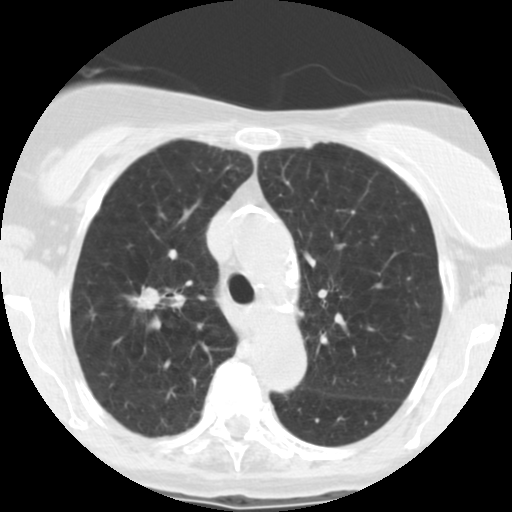
Low-dose screening chest CT, axial slice, baseline screening round, lung window (W 1500 / L -600 HU), slice 179 of 246 in the series, 512 × 512 image matrix. Female, age 67 years at enrolment. Former smoker at enrolment.
Expert-annotated lung lesion, bounding box <114,278,175,319> (left, top, right, bottom; pixels). The screening reader recorded 6 non-calcified nodules or masses ≥4 mm on this exam; which of them this box marks is not recorded. Participant outcome: lung cancer diagnosed 15 days after this screen — adenocarcinoma, NOS, right upper lobe, moderately differentiated (G2), stage IA (AJCC 6th edition), 14 mm at pathology.